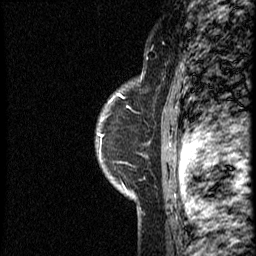
Breast MRI (dynamic contrast-enhanced), one sagittal slice; slice 31 of 40 in the series (ordered by position); dynamic contrast-enhanced study with each time point stored as its own series, time point 2 of 4 at this slice position (early post-contrast, ordered by acquisition time); 1.5 T; TE 4.2 ms, TR 18.8 ms; 256 × 256 image matrix, field of view 200 × 200 mm. Female patient. From the clinical record (not read from this slice): setting: breast cancer imaged before/during neoadjuvant chemotherapy; receptor status: HER2-positive.
Structures marked on this image (semi-automatic segmentation, software-assisted and operator-edited):
- analysis volume of interest (the breast-tissue region the enhancement analysis was run in; not a lesion): bounding box (x1, y1, x2, y2) in pixels: (97, 79, 165, 153)
- tumour enhancement mask (voxels above the 100 % enhancement threshold inside the analysis volume of interest): (102, 94, 125, 136)